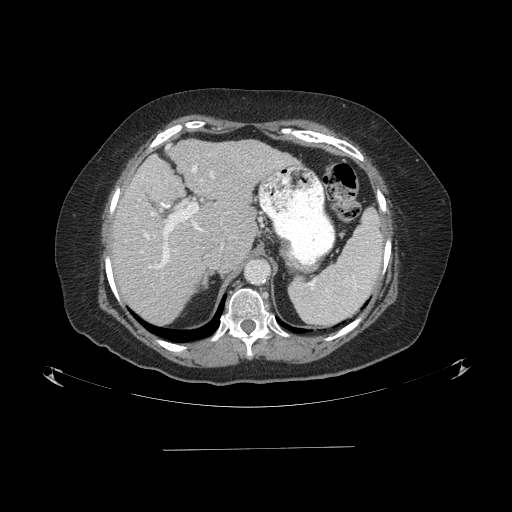
Contrast-enhanced abdominal CT (liver protocol), one axial slice; position 59 of 103 along the scan axis; reconstruction kernel STANDARD; one of 2 acquisitions stored at this slice position; soft-tissue window (W 400 / L 40 HU); 2.5 mm slice thickness; 512 × 512 image matrix, field of view 500 × 500 mm. Case-level facts recorded for this patient, not image findings: diagnosis: hepatocellular carcinoma (patient treated with transarterial chemoembolisation; whether this scan precedes or follows treatment is not stated here); TNM stage (as recorded): Stage-IIIA; Child-Pugh class: A; tumour differentiation: poorly differentiated; tumour nodularity: multinodular.
Structures marked on this image (semi-automatic segmentation, software-assisted and operator-edited):
- abdominal aorta: bounding box [x1, y1, x2, y2] px = [246, 261, 268, 283]
- liver parenchyma outside the tumour (the mass and vessels are separate outlines, so this box may not span the whole liver): [112, 140, 294, 324]
- liver vessels: [141, 165, 223, 269]